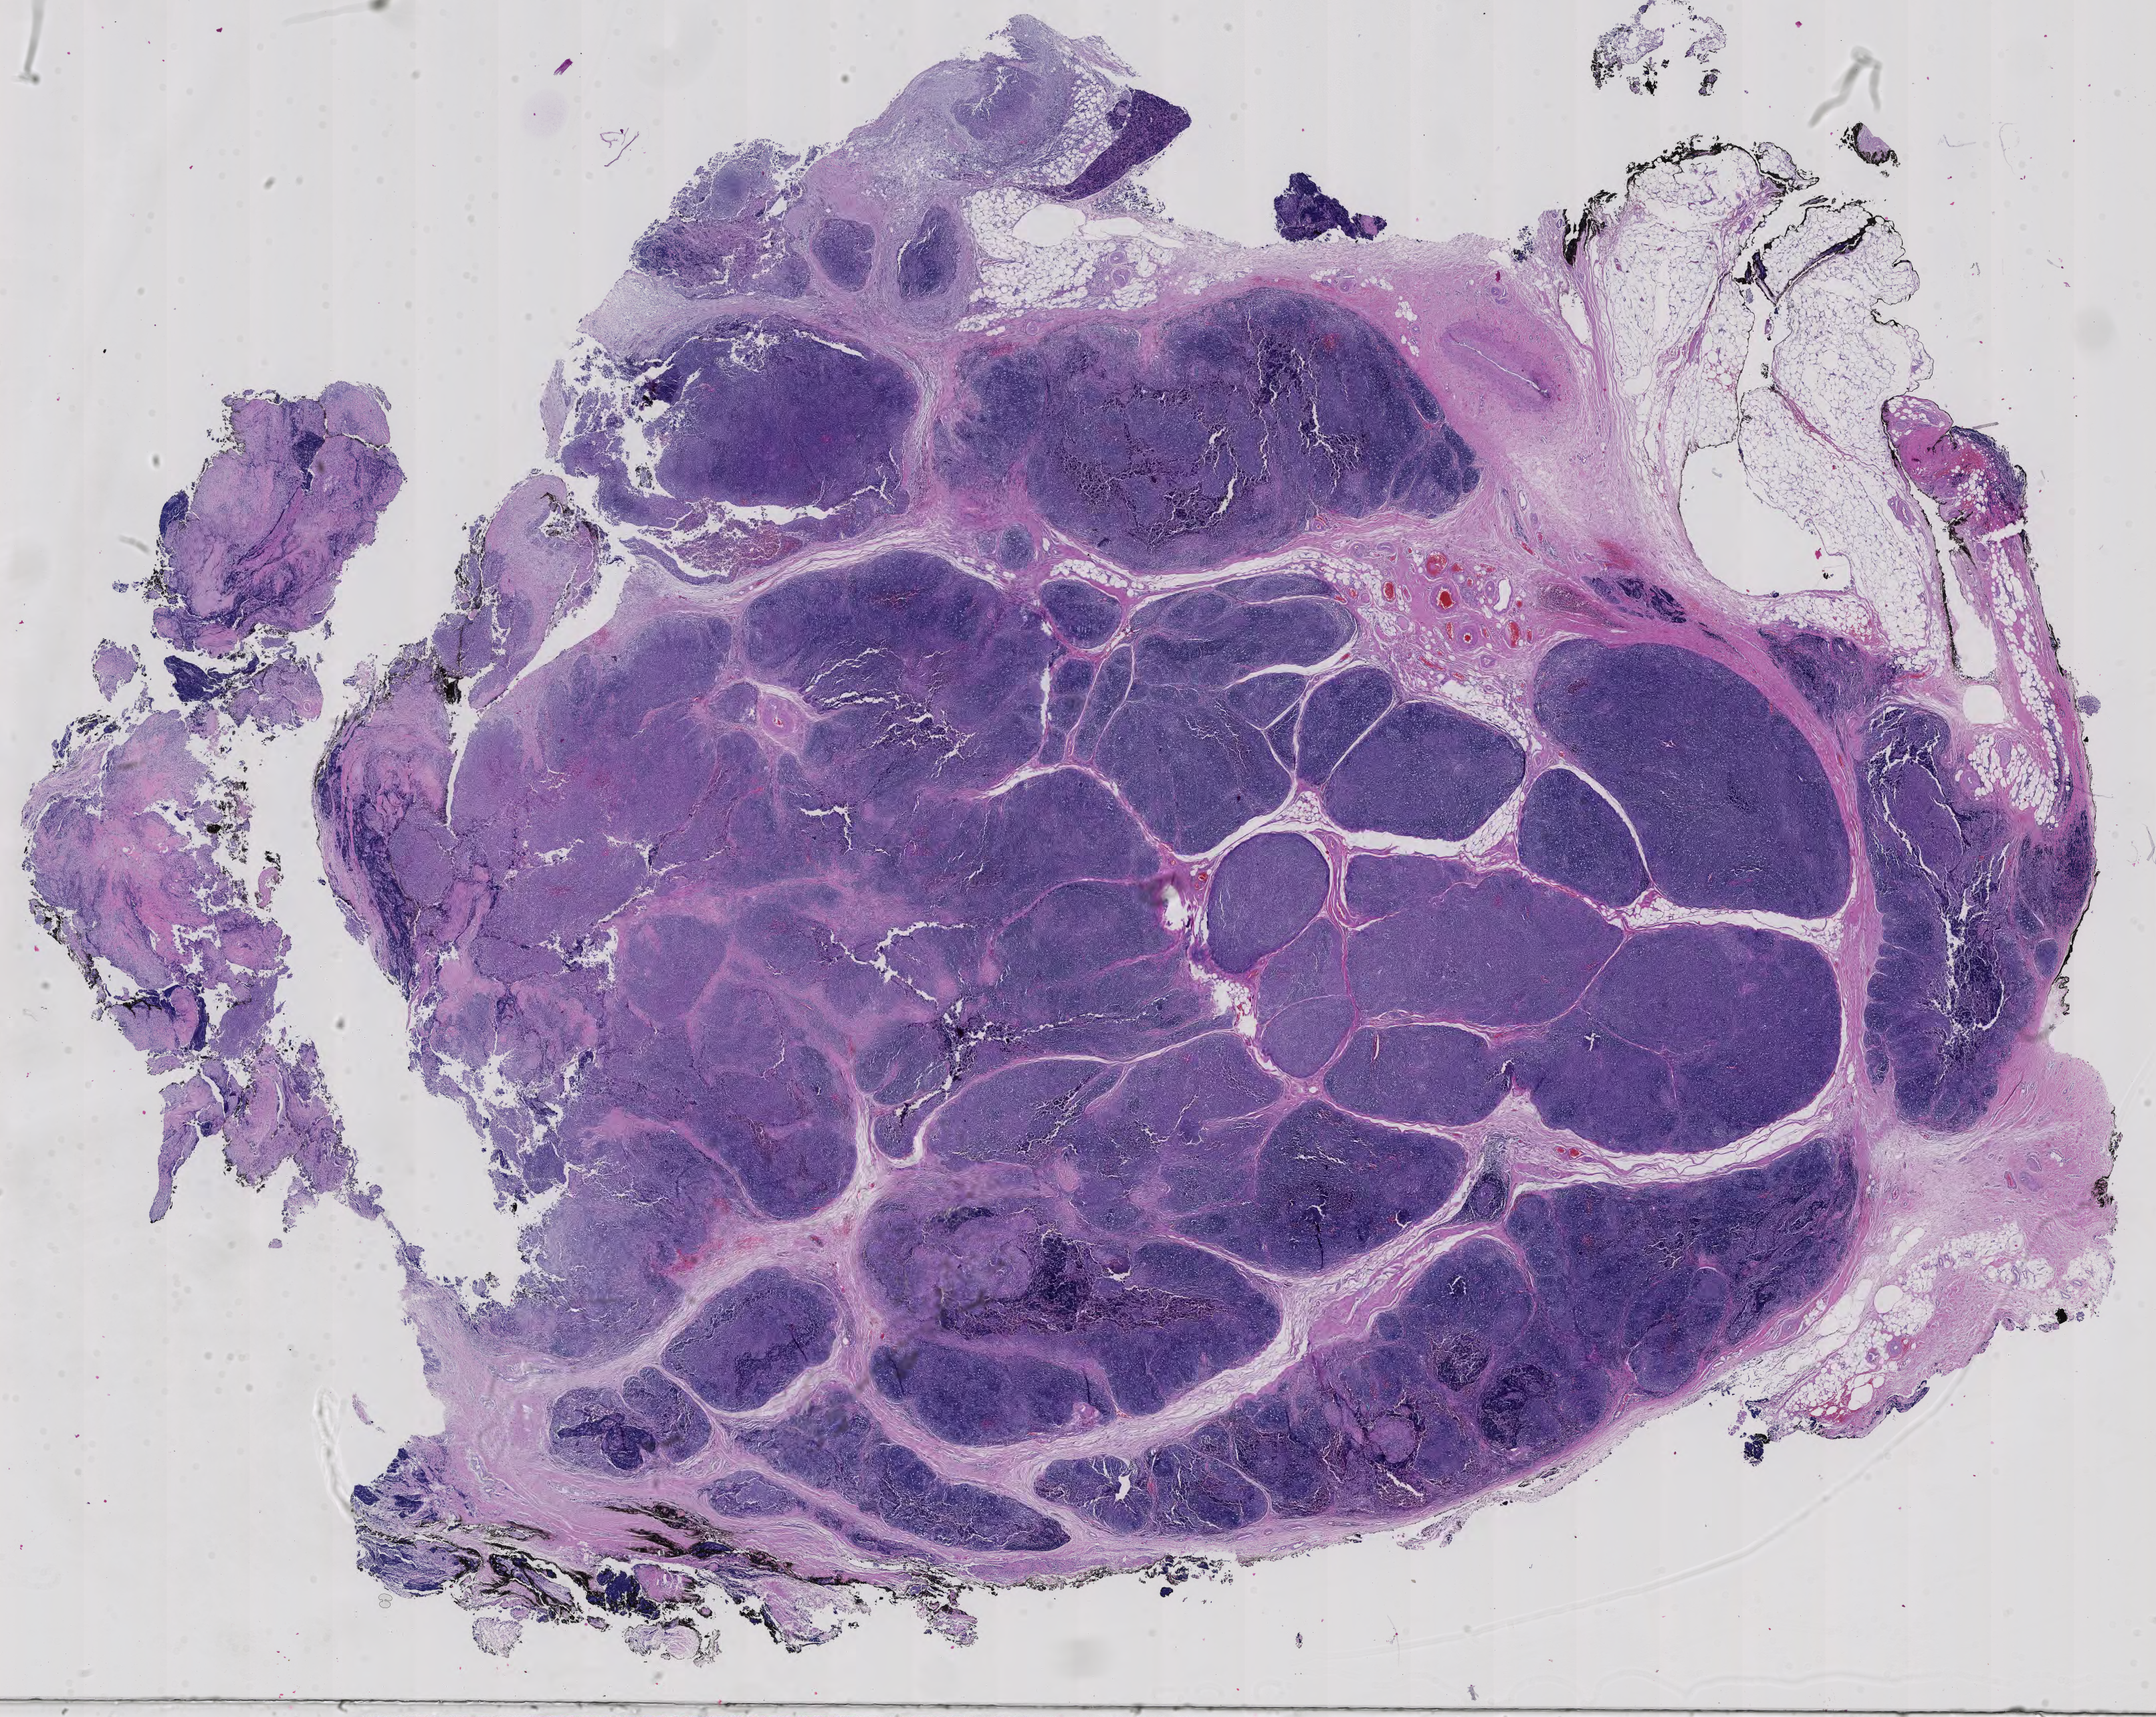
Digitized H&E tissue section (whole slide), low-resolution overview of the scanned area, about 23.5 x 18.7 mm. Formalin-fixed paraffin-embedded (FFPE) diagnostic section. Primary tumour sample from the thymus. Male, age 46 years at initial diagnosis.
* pathologic diagnosis: Thymoma, type AB, malignant (anterior mediastinum)